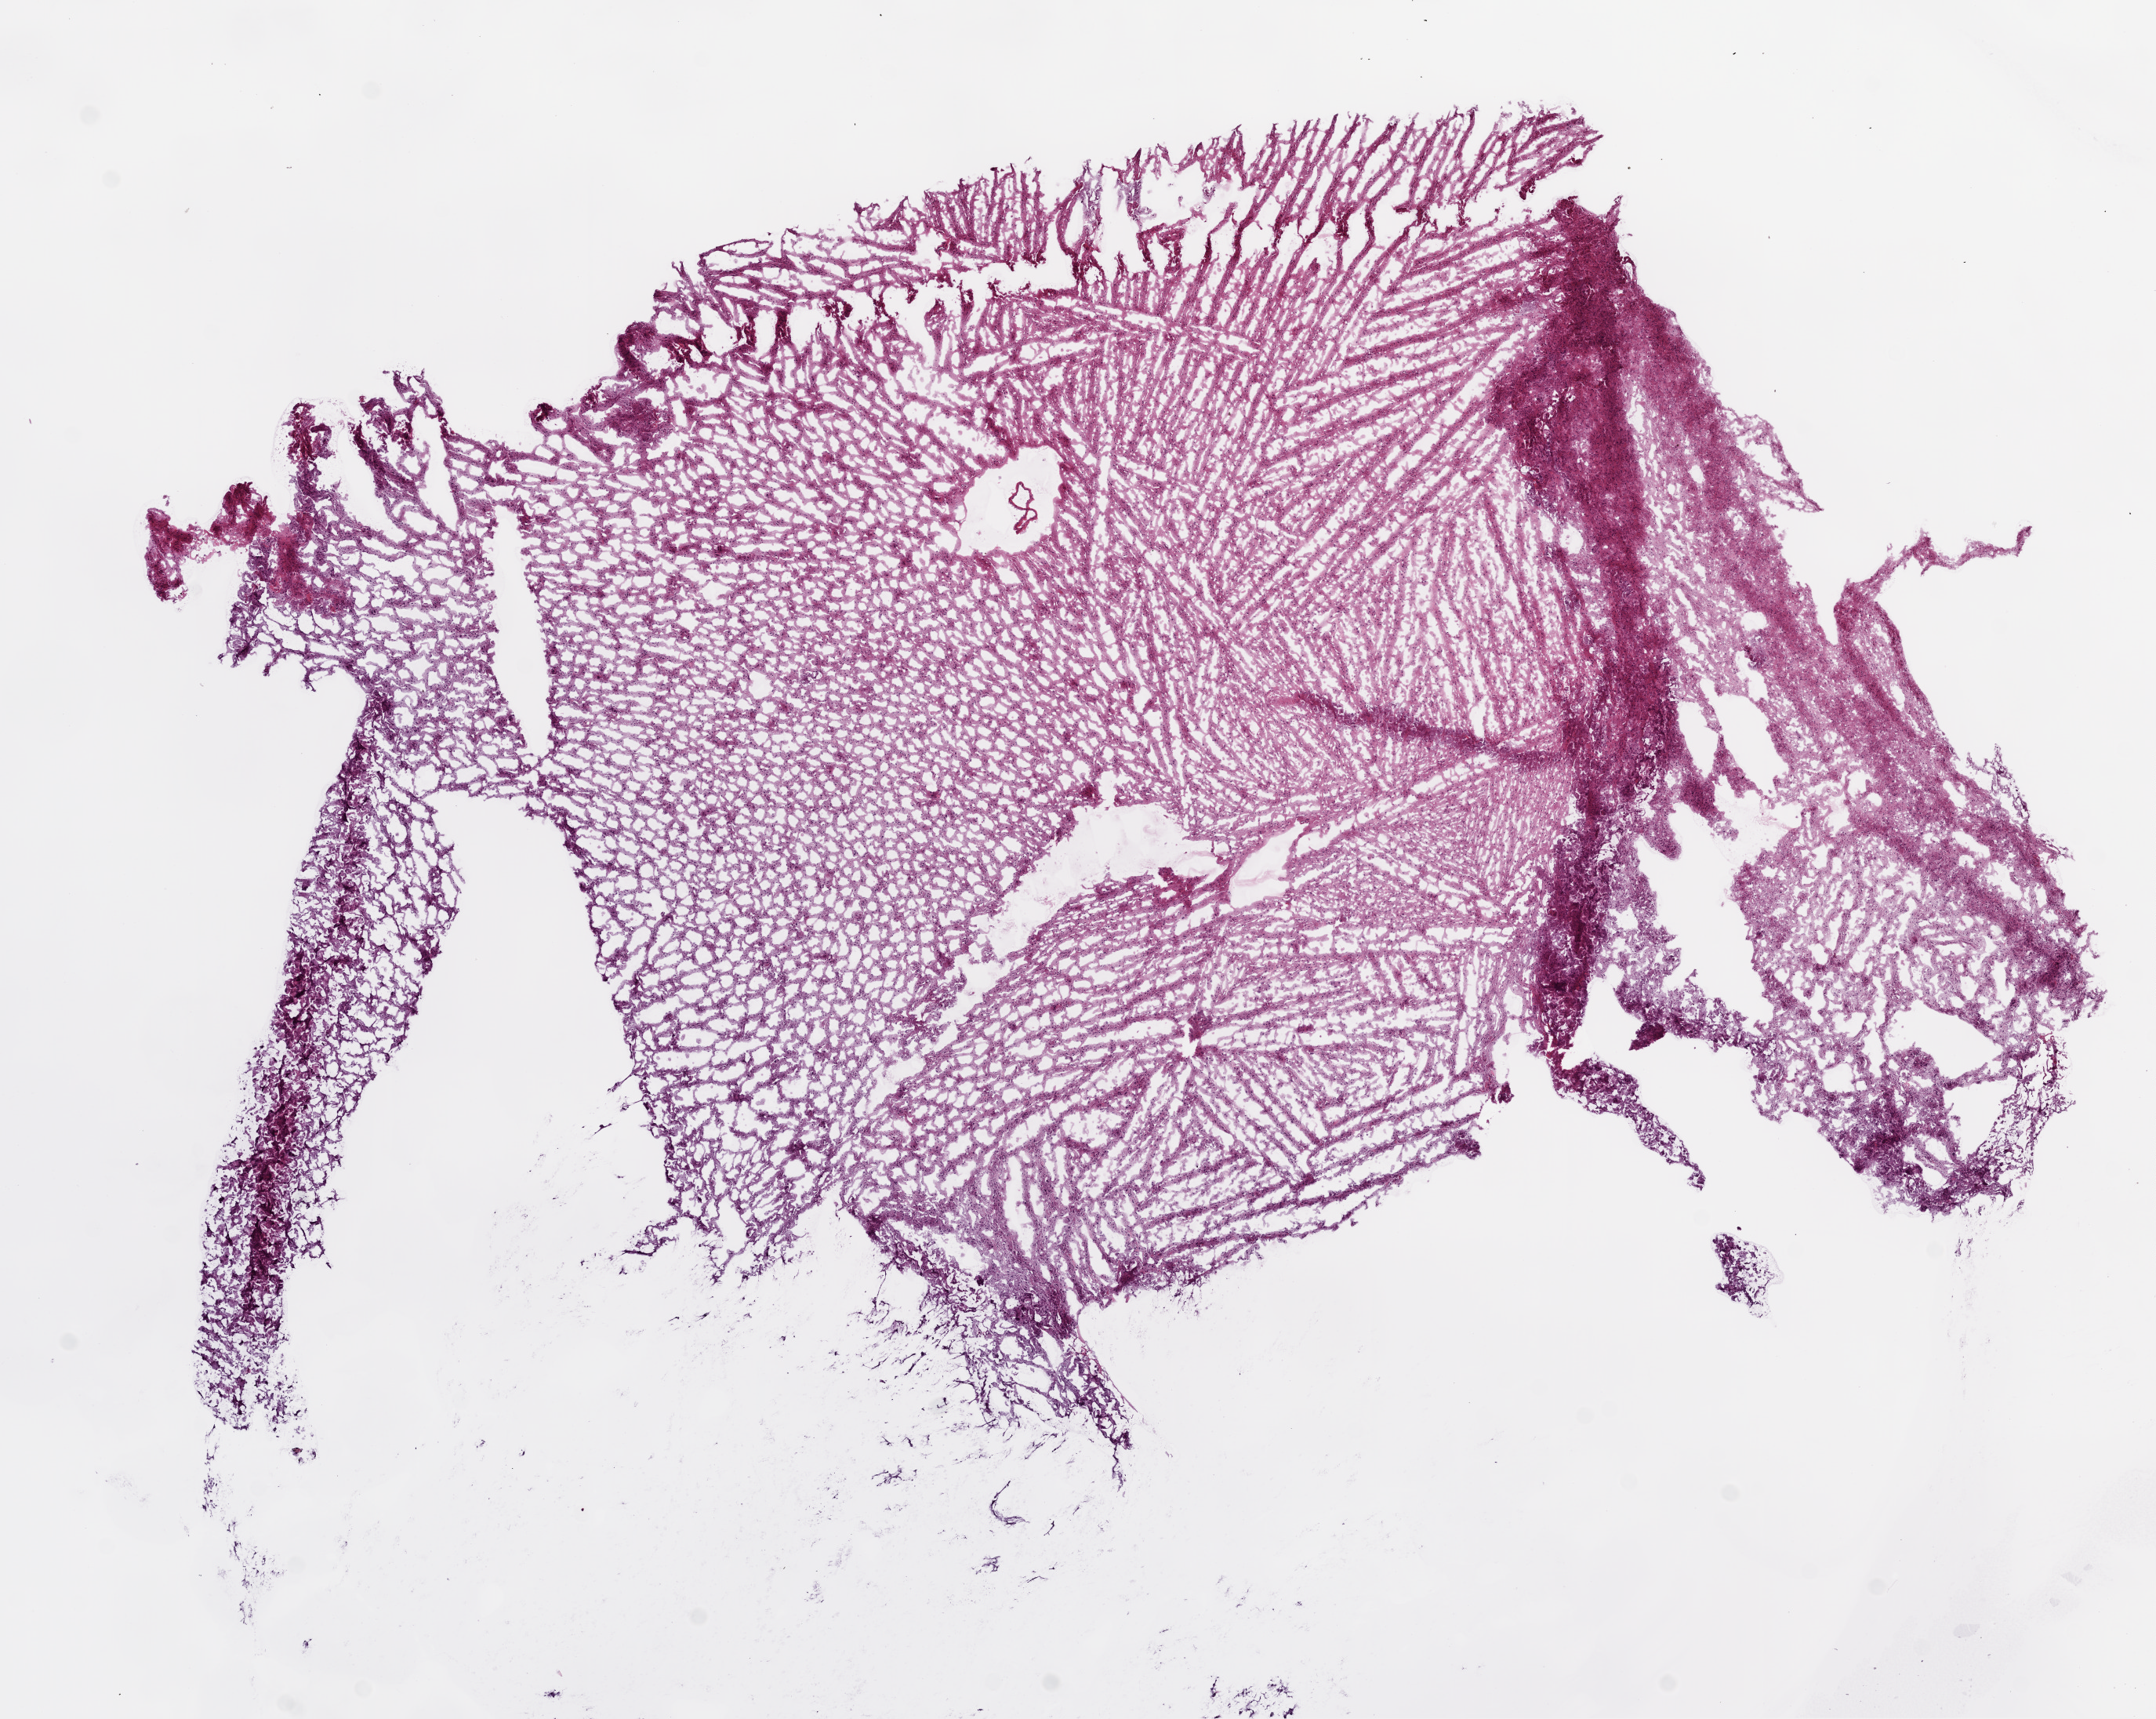
Whole-slide histology image, H&E — a low-resolution overview of the entire scanned area, about 11.0 x 8.8 mm (acquisition: 20x scan); frozen section; brain, primary tumour sample. Male patient; age at initial diagnosis 30 years. Histologic grade: G3 (poorly differentiated). Composition of this section per pathologist review: tumour cells 100%, tumour nuclei 65%, normal cells 0%, stromal cells 0%, necrosis 0%.
Pathologic diagnosis: Mixed glioma.